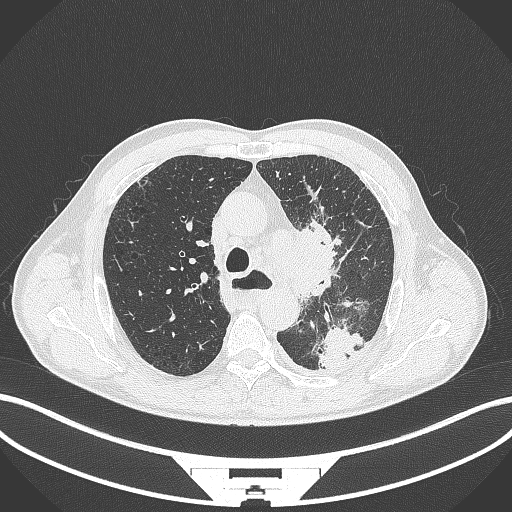
Chest CT, one axial slice; position 271 of 411 along the scan axis; reconstruction kernel B70f; 120 kVp; lung window (W 1500 / L -600 HU); 1 mm slice thickness; 512 × 512 image matrix, field of view 400 × 400 mm. Patient: male, 57 years. Case-level facts recorded for this patient, not image findings: clinical TNM (as recorded): T2a N1 M0.
Outlined on this slice (rectangle marked by the reading radiologist):
- lung tumour (recorded histology: squamous cell carcinoma): bounding box [x1, y1, x2, y2] px = [290, 224, 340, 300]